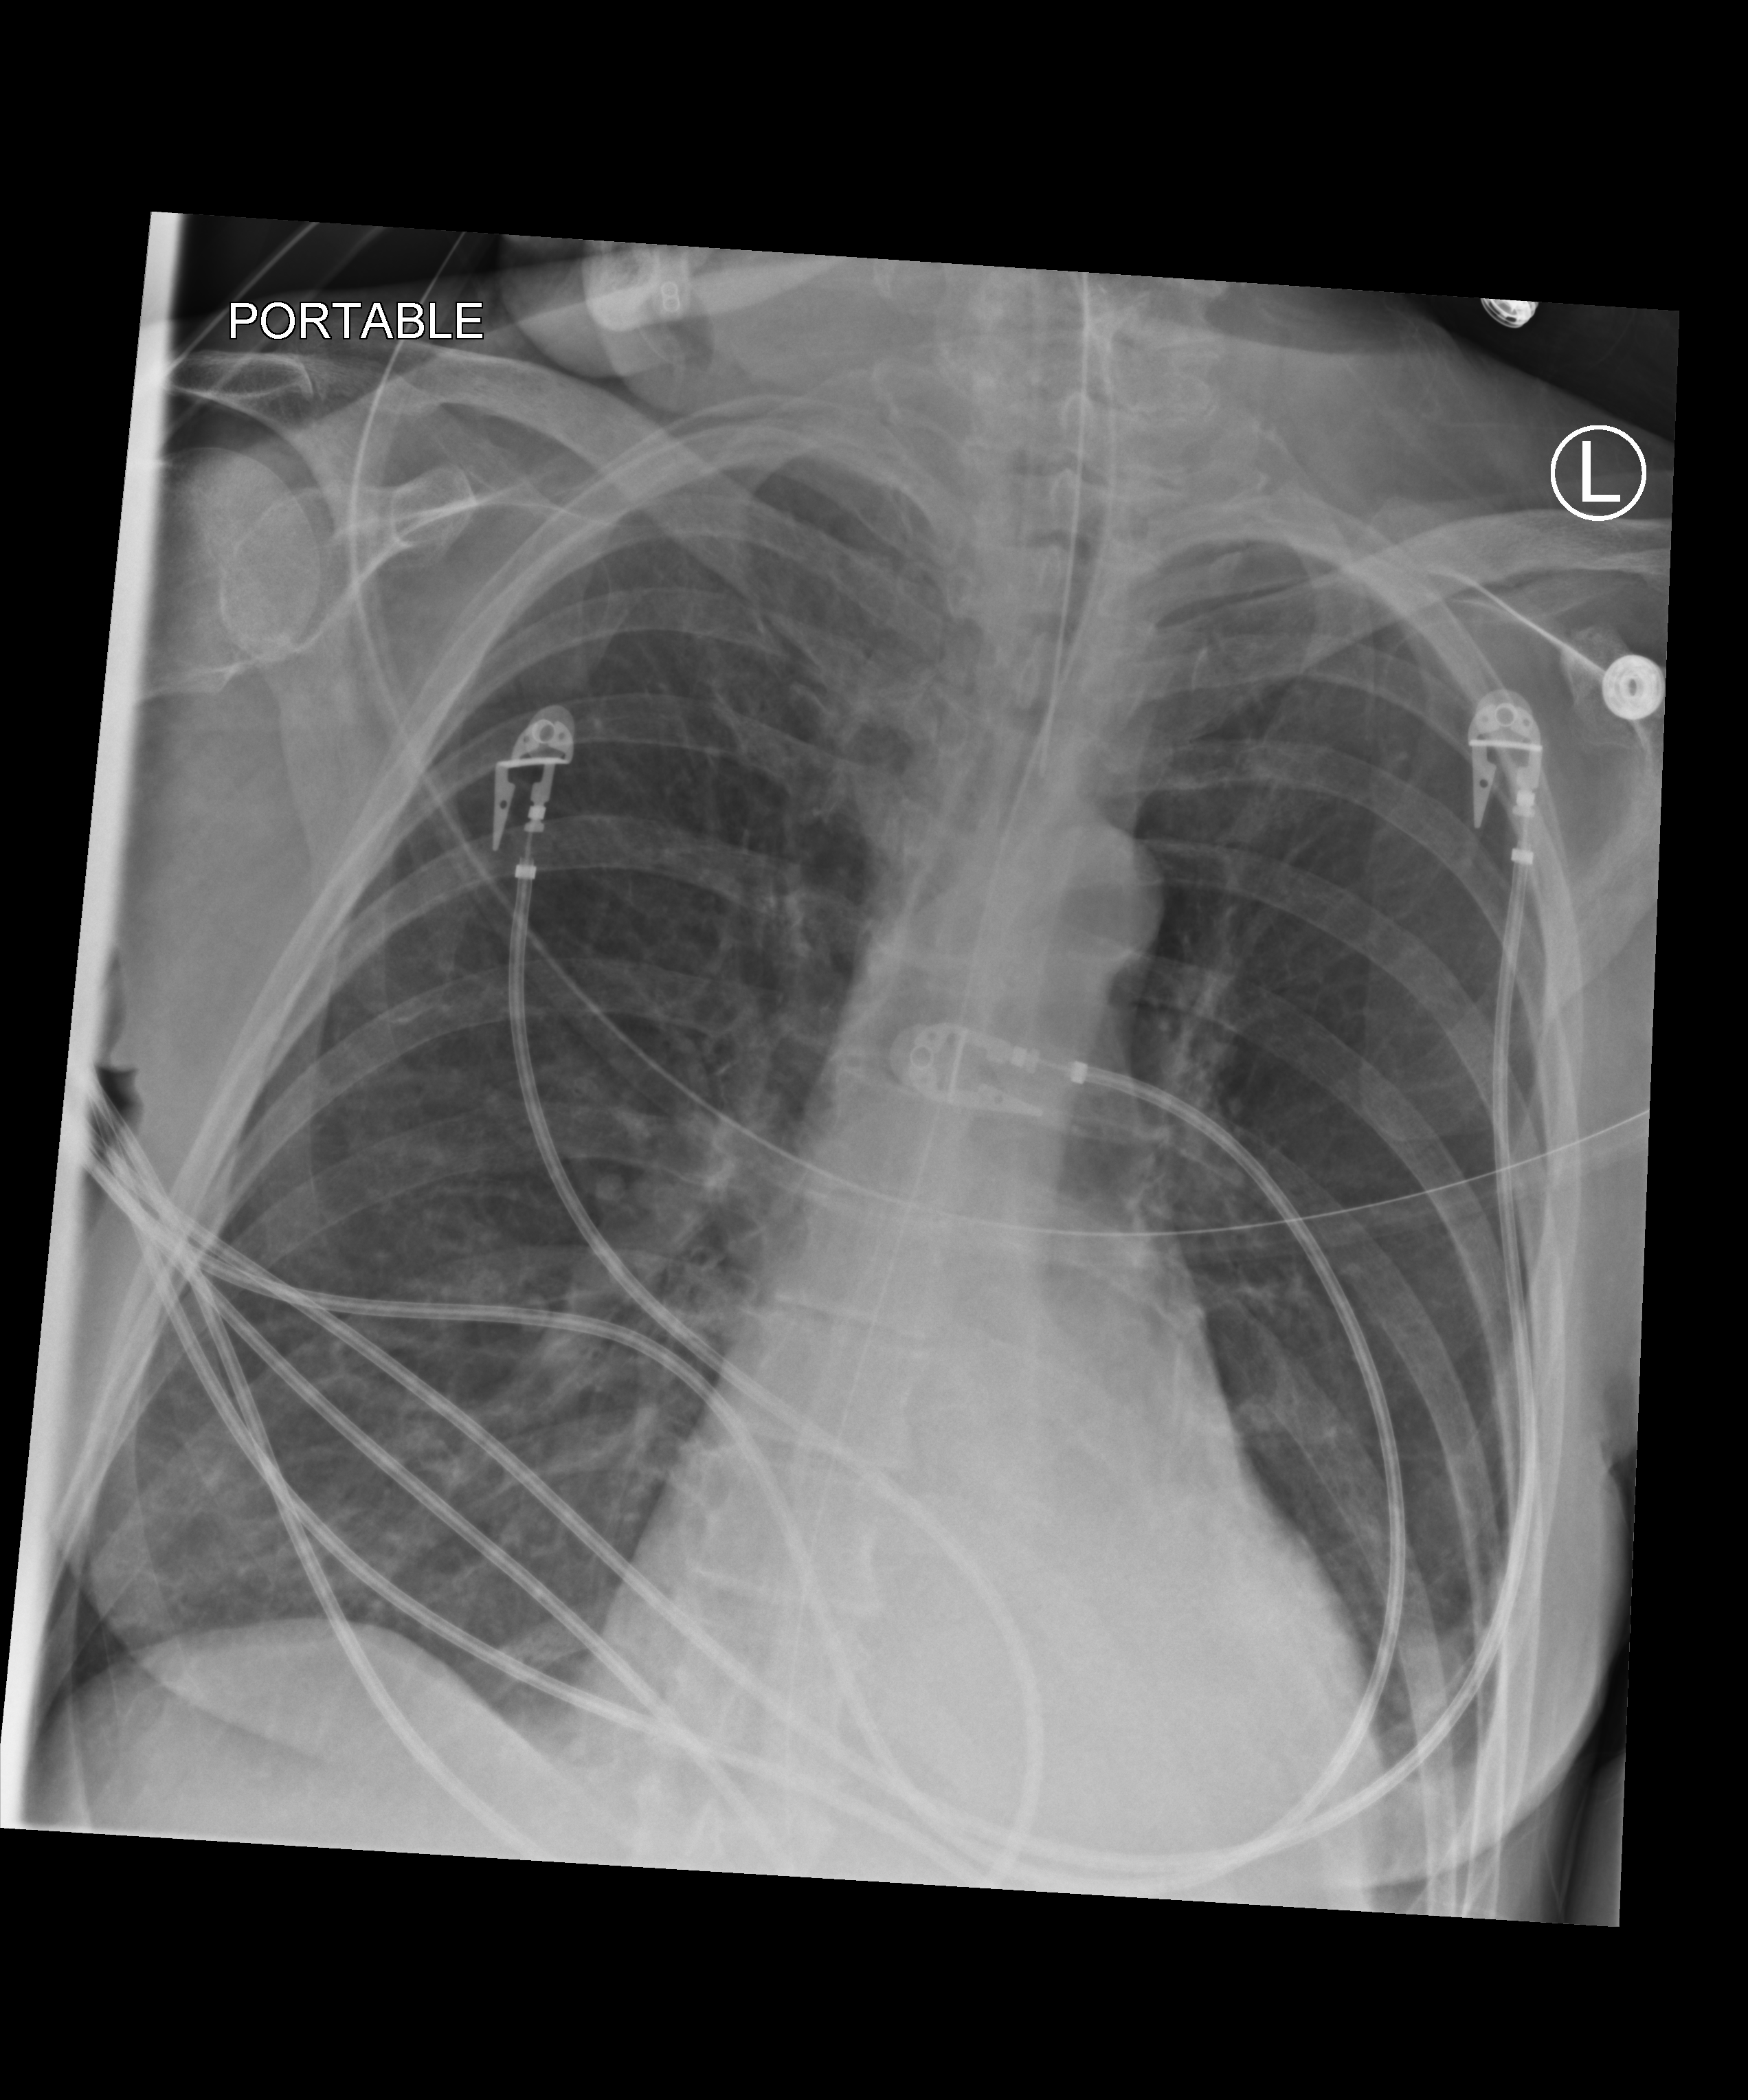
Chest X-ray (portable), anteroposterior (AP) projection. Patient hospitalised with COVID-19; female, aged 60–74 years.
Hospital-stay facts (about this admission, not read from this image; timing relative to this image not recorded):
- mechanically ventilated during this hospital stay: yes